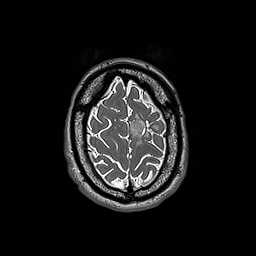
Brain MRI from a brain-tumour surgery series, one axial slice; slice 42 of 192 in the series (ordered by position); 1 mm slice thickness; 256 × 256 image matrix, field of view 250 × 250 mm. From the clinical record (not read from this slice): histopathology: Oligodendroglioma; WHO grade: 3; IDH mutation: yes.
Structures marked on this image (expert manual segmentation):
- tumour: bounding box <130,117,159,145> (left, top, right, bottom; pixels)